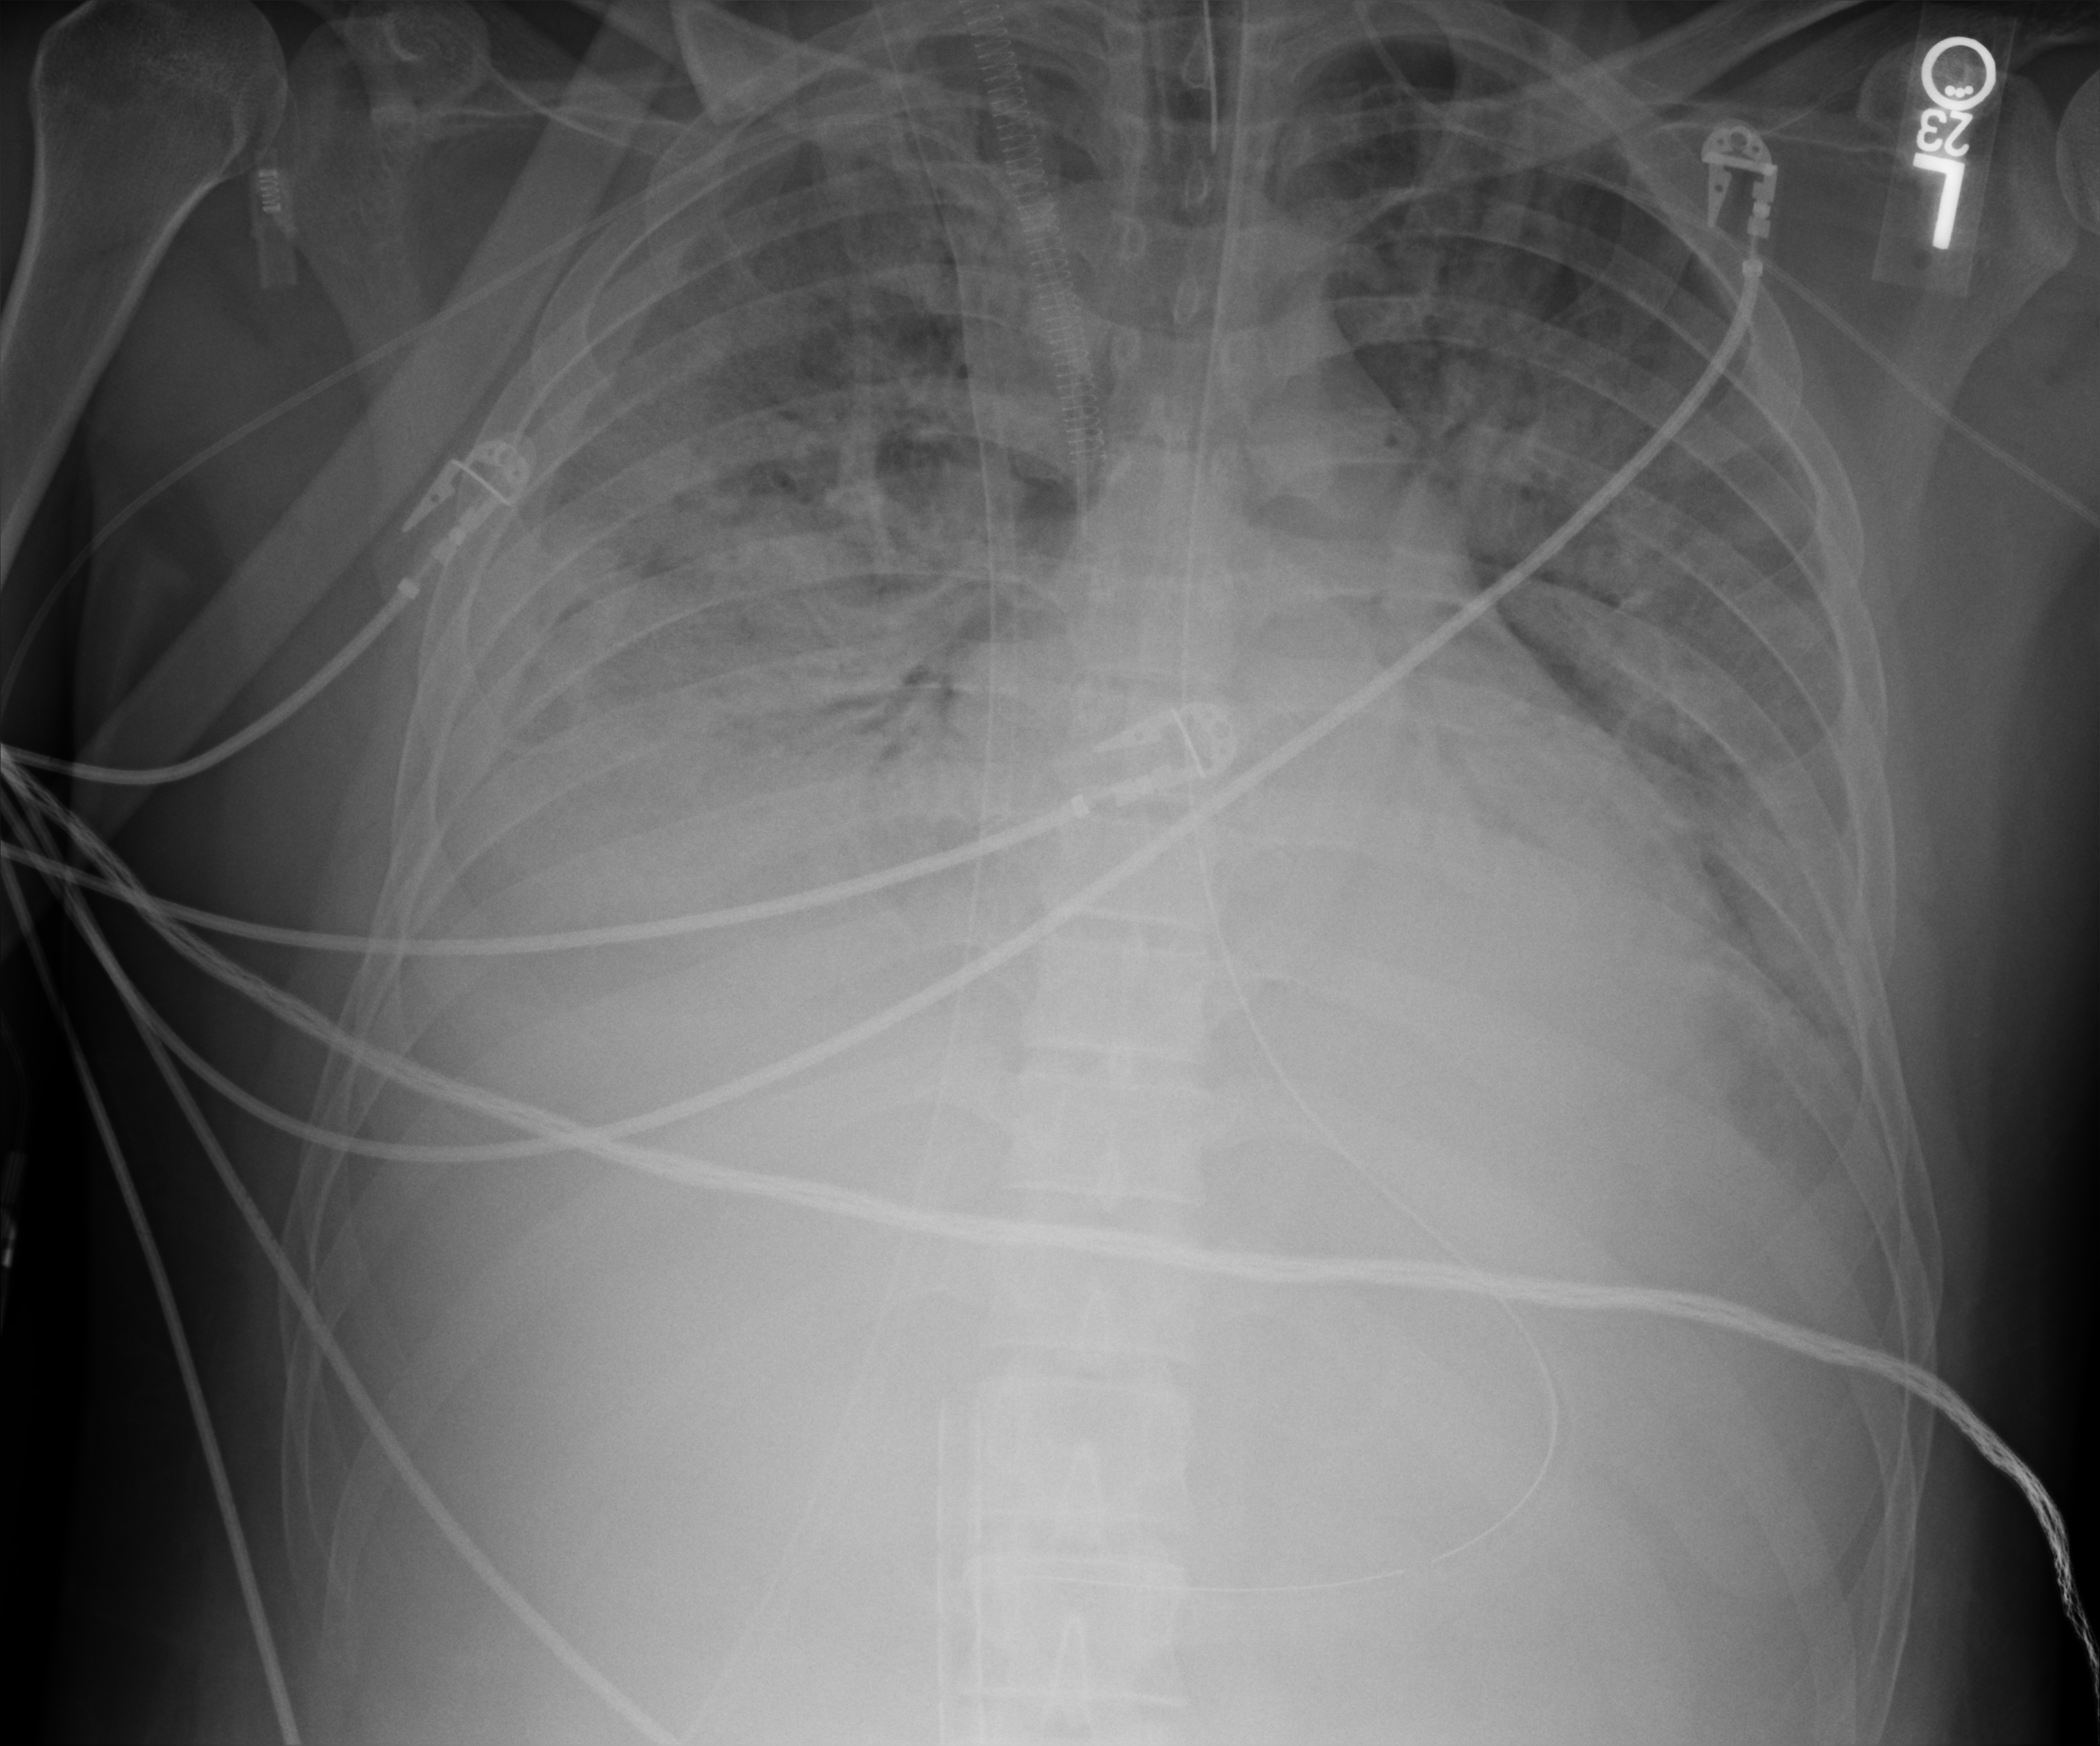
Chest X-ray (portable), anteroposterior (AP) projection. Patient hospitalised with COVID-19, aged 18–59 years.
Admission-level facts for this patient (not findings on this image; timing relative to this image not recorded):
- smoking status (admission record): never